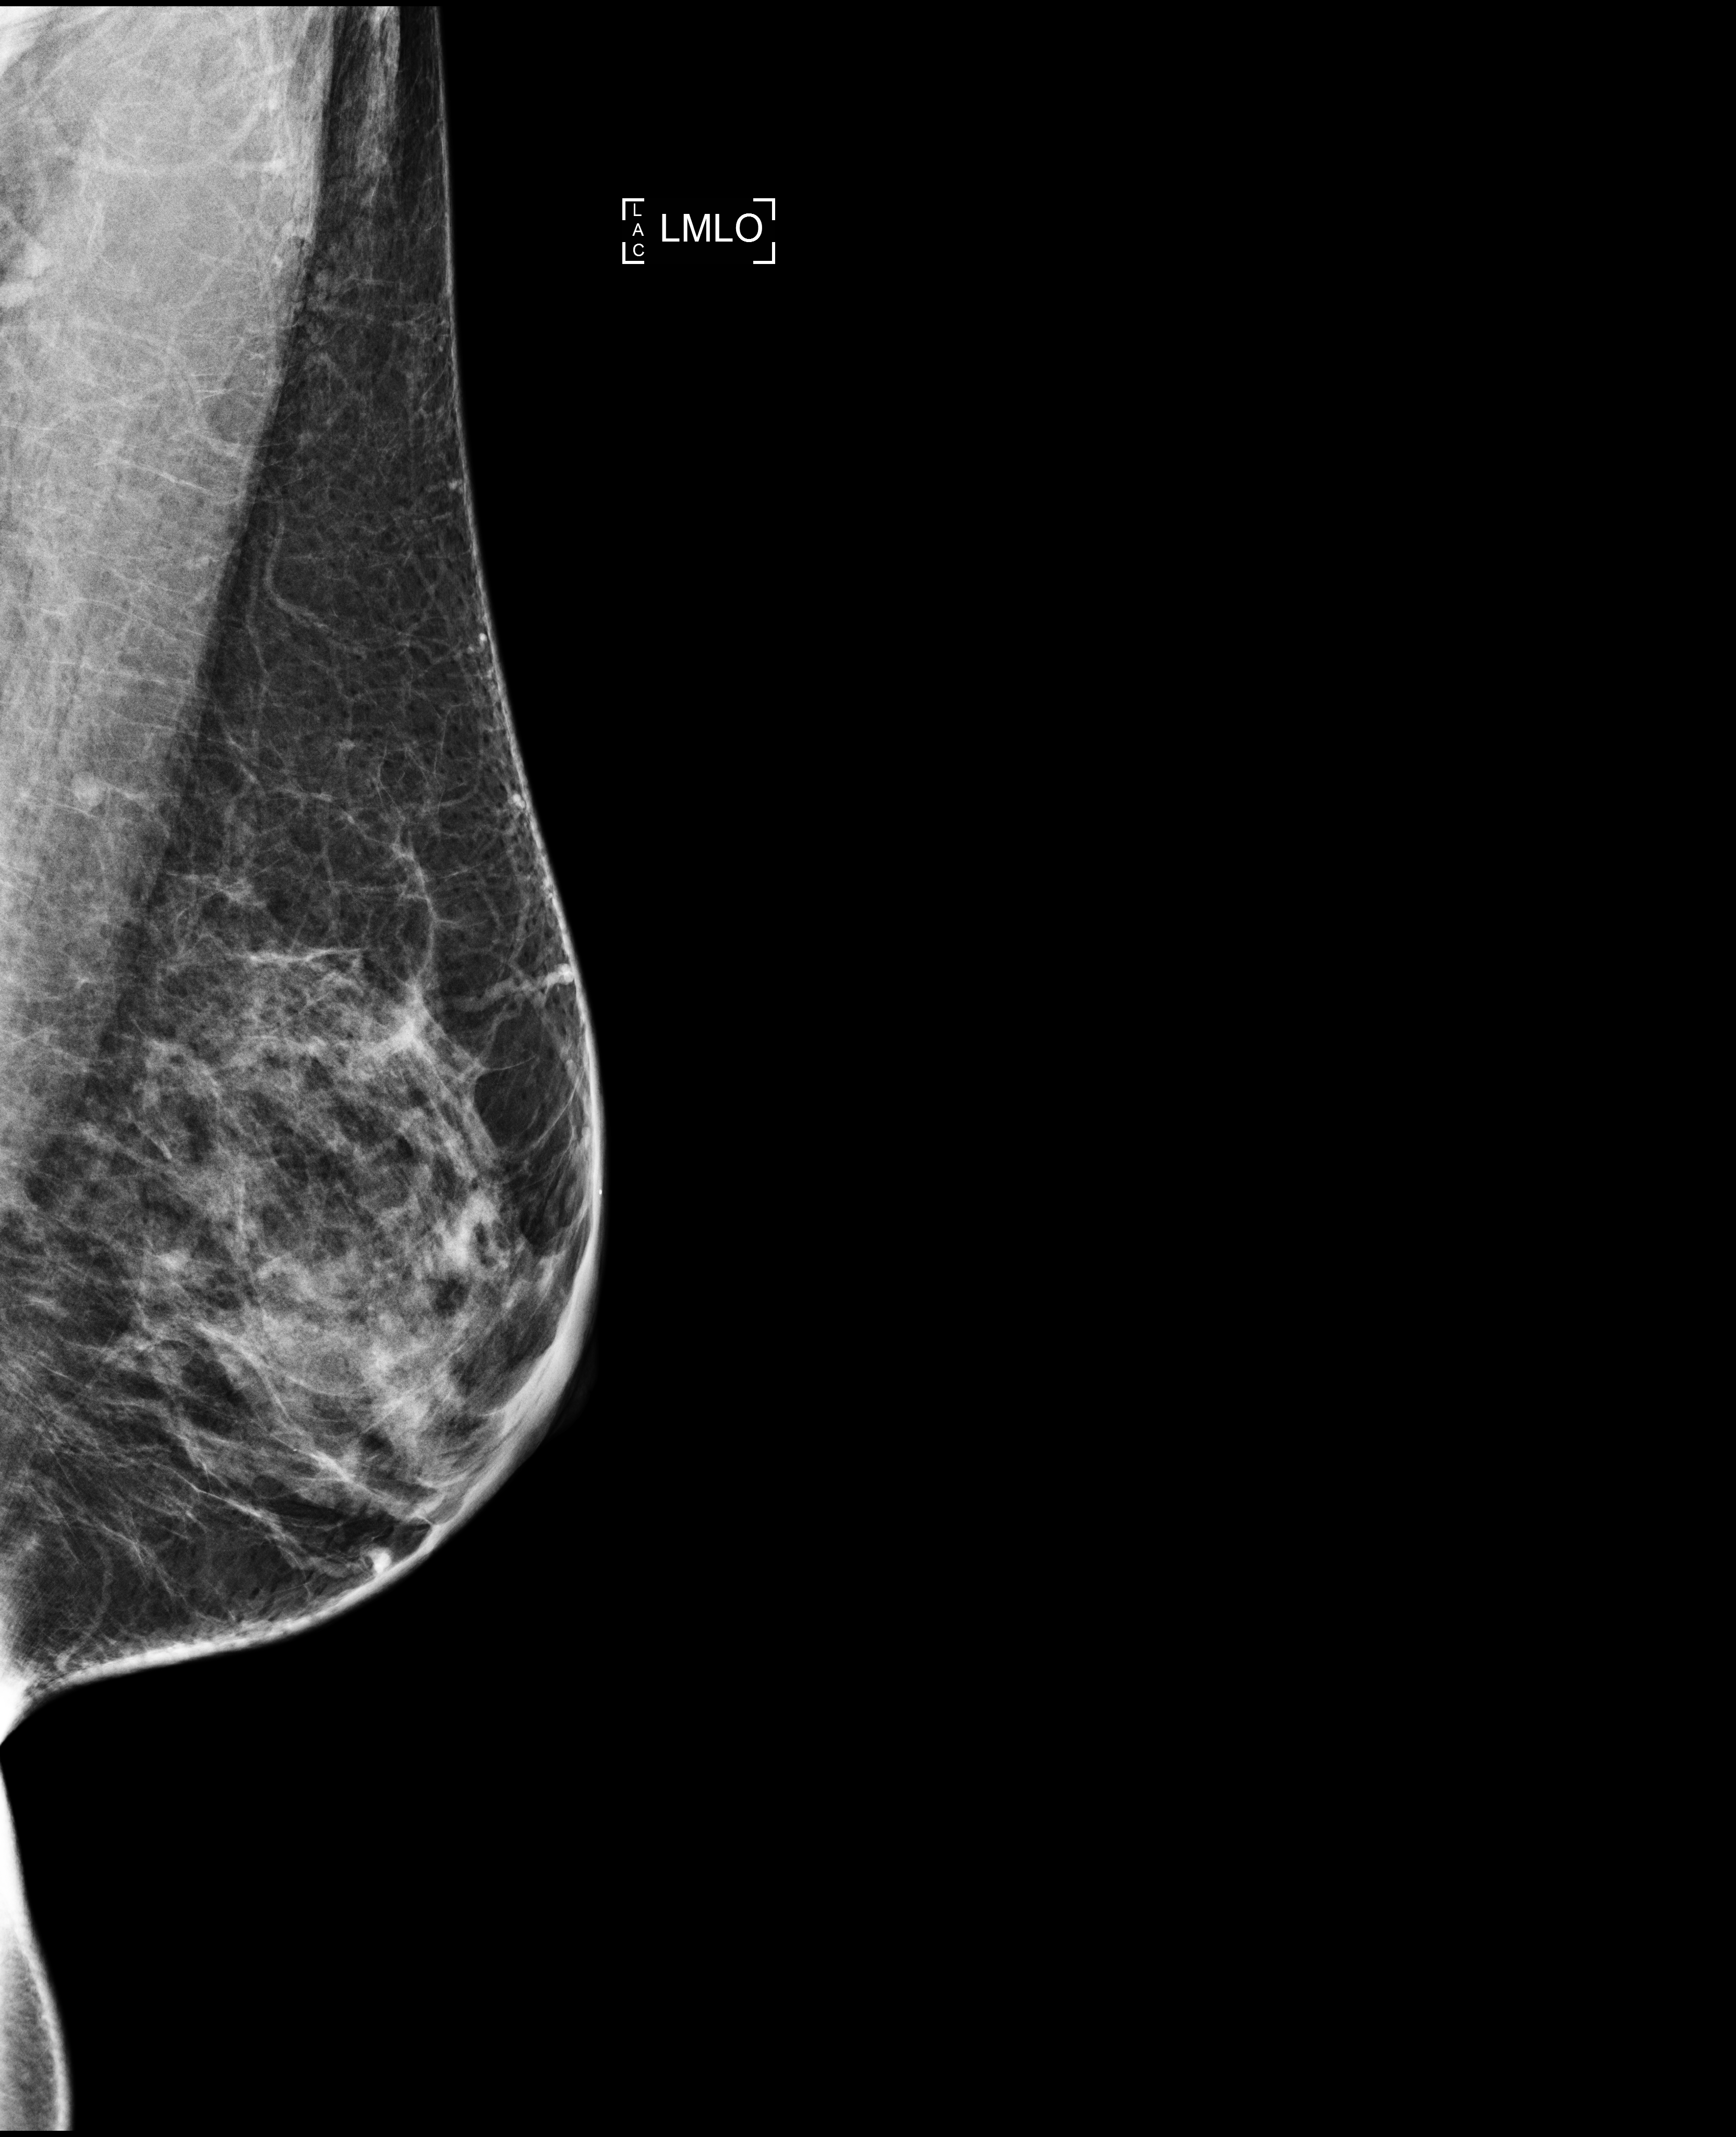
Annual screening mammography examination; system: Selenia Dimensions. Patient aged 45 years (female).
Image type: full-field digital mammogram. Breast: left. Projection: MLO view.